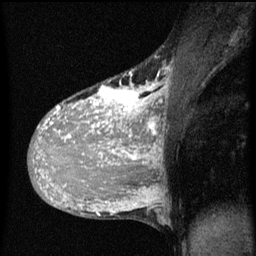
Breast MRI (dynamic contrast-enhanced), one sagittal slice; position 30 of 60 along the scan axis; dynamic contrast-enhanced series, image 2 of 3 at this slice position (ordered by acquisition); 1.5 T; TE 4.2 ms, TR 8 ms; 2 mm slice thickness; 256 × 256 image matrix. Patient: female, 36 years.
Annotated regions visible in this slice (semi-automatic segmentation, software-assisted and operator-edited):
- analysis volume of interest (the breast-tissue region the enhancement analysis was run in; not a lesion): bounding box (x1, y1, x2, y2) in pixels: (32, 70, 167, 161)
- tumour enhancement mask (voxels above the 70 % enhancement threshold inside the analysis volume of interest): (32, 80, 167, 161)